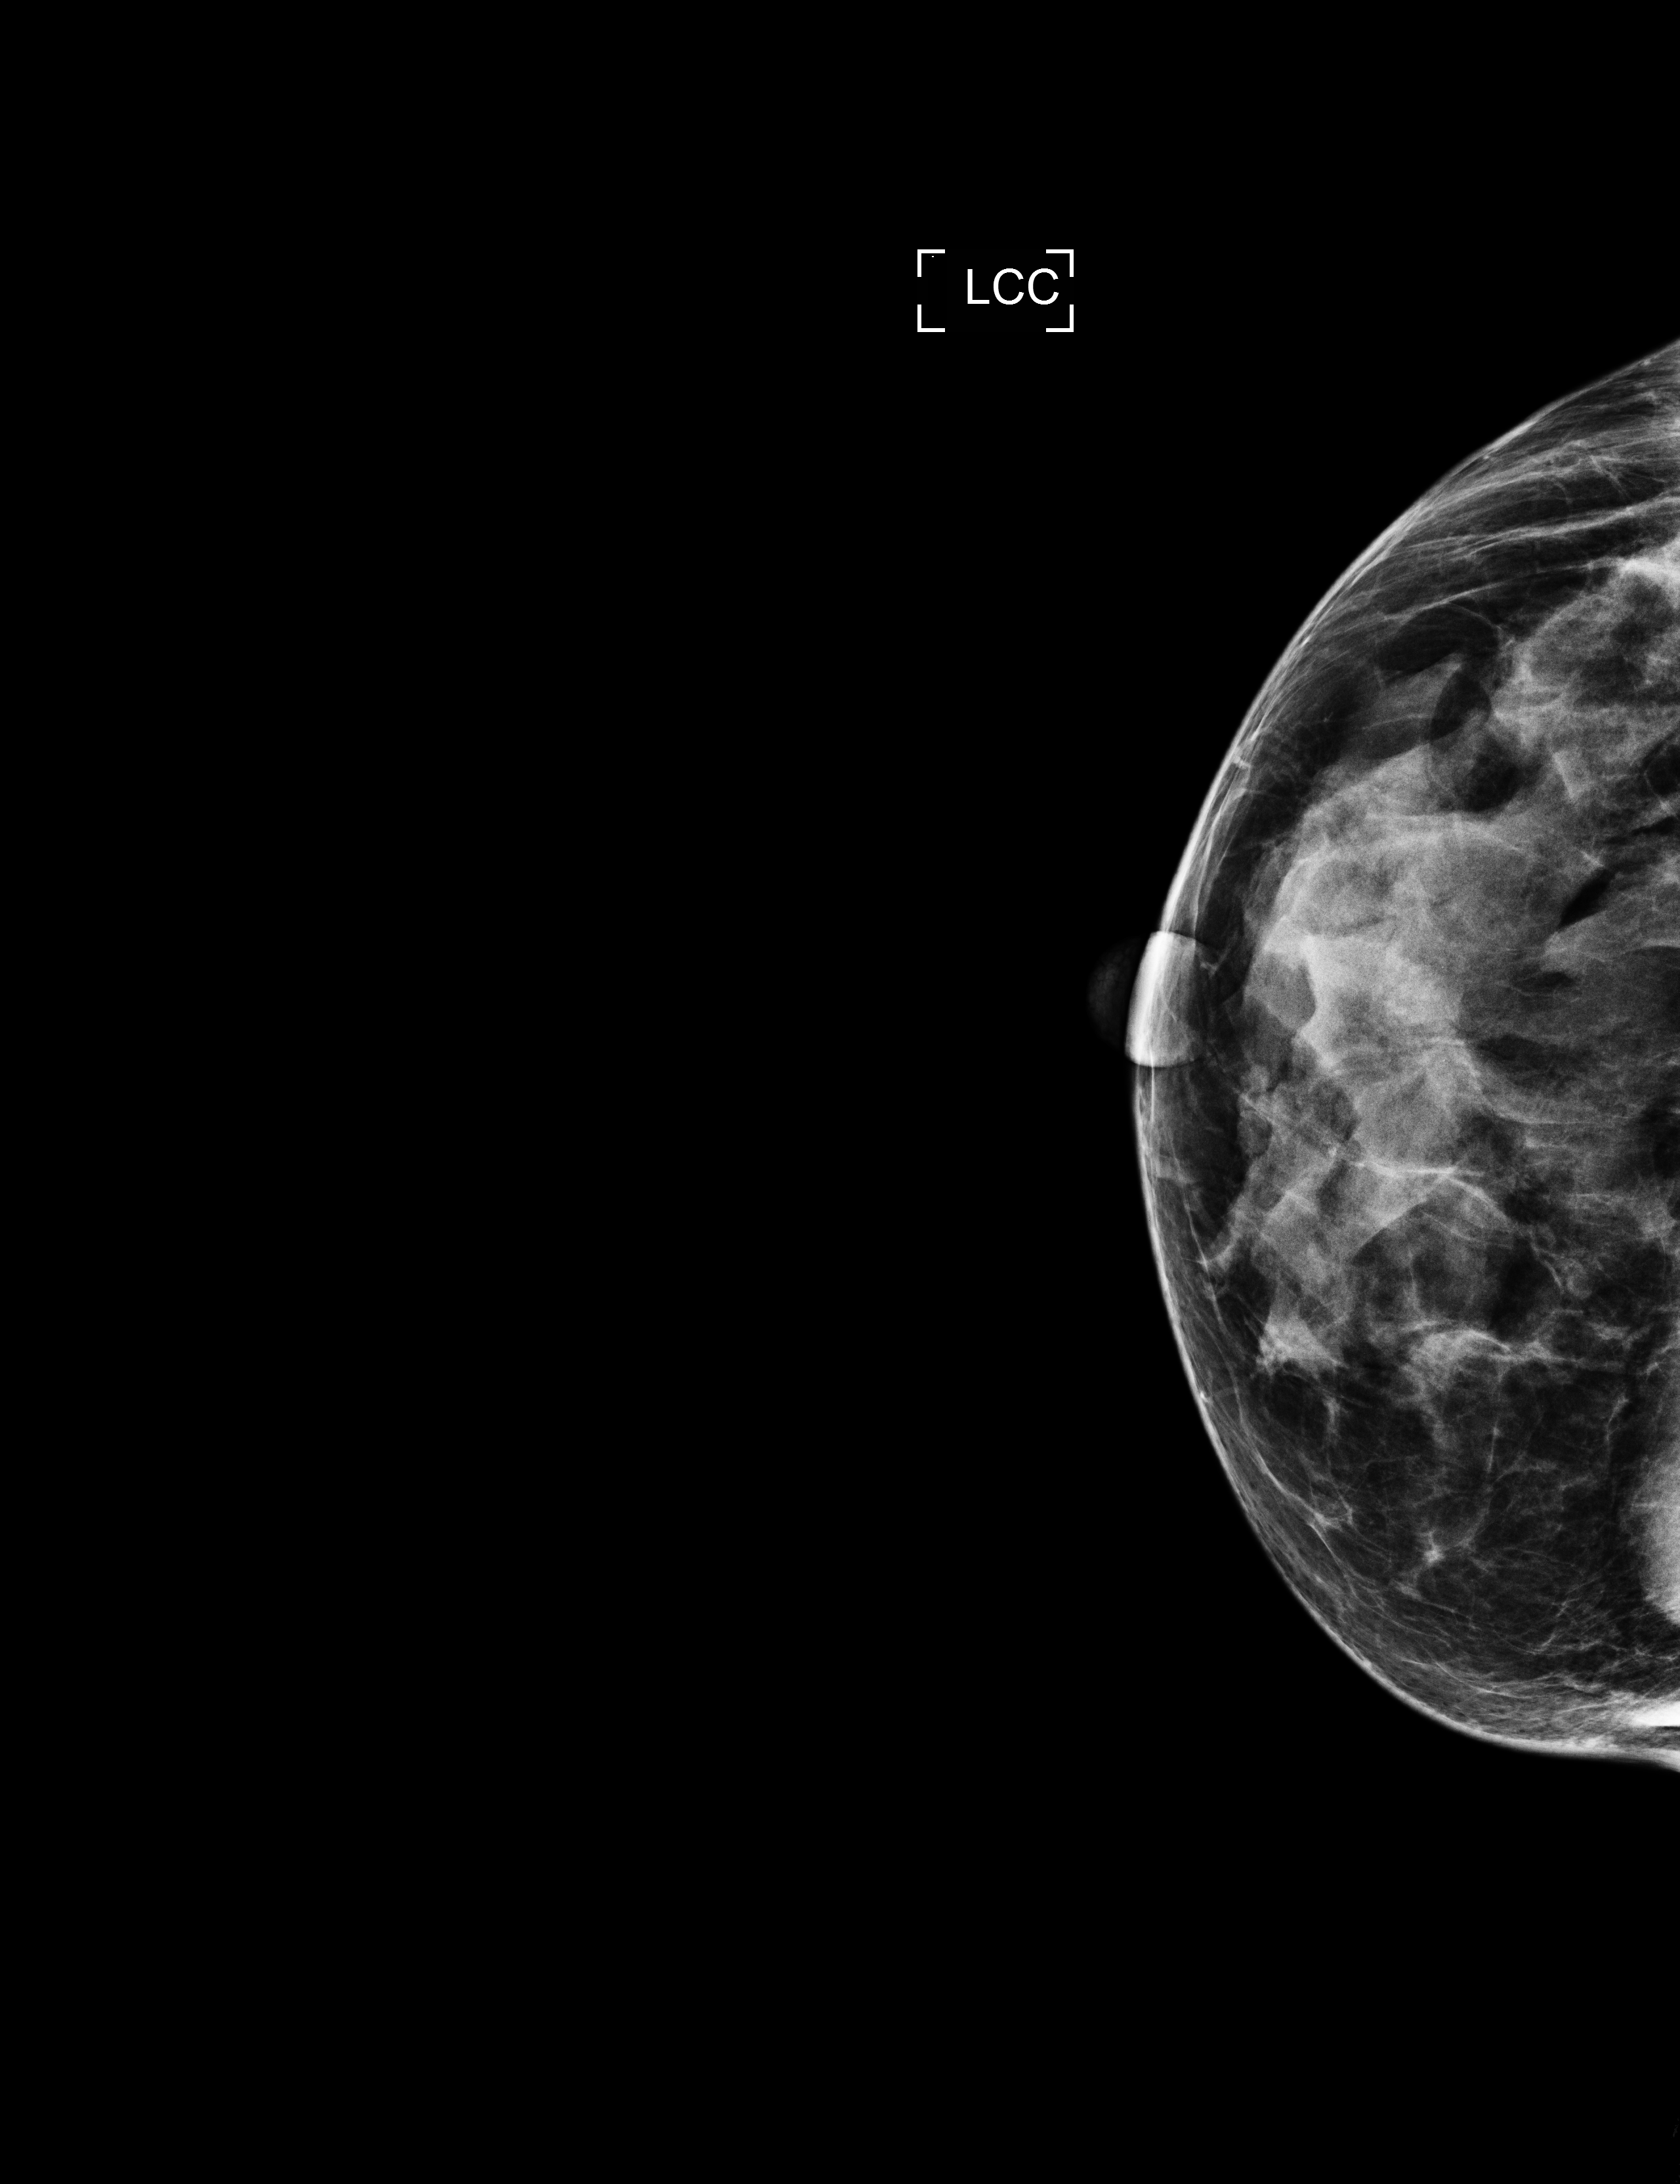
Screening examination; compressed breast thickness 25 mm. Female patient, age 54 years.
Image type: full-field digital mammogram. Breast: left. Projection: CC view.